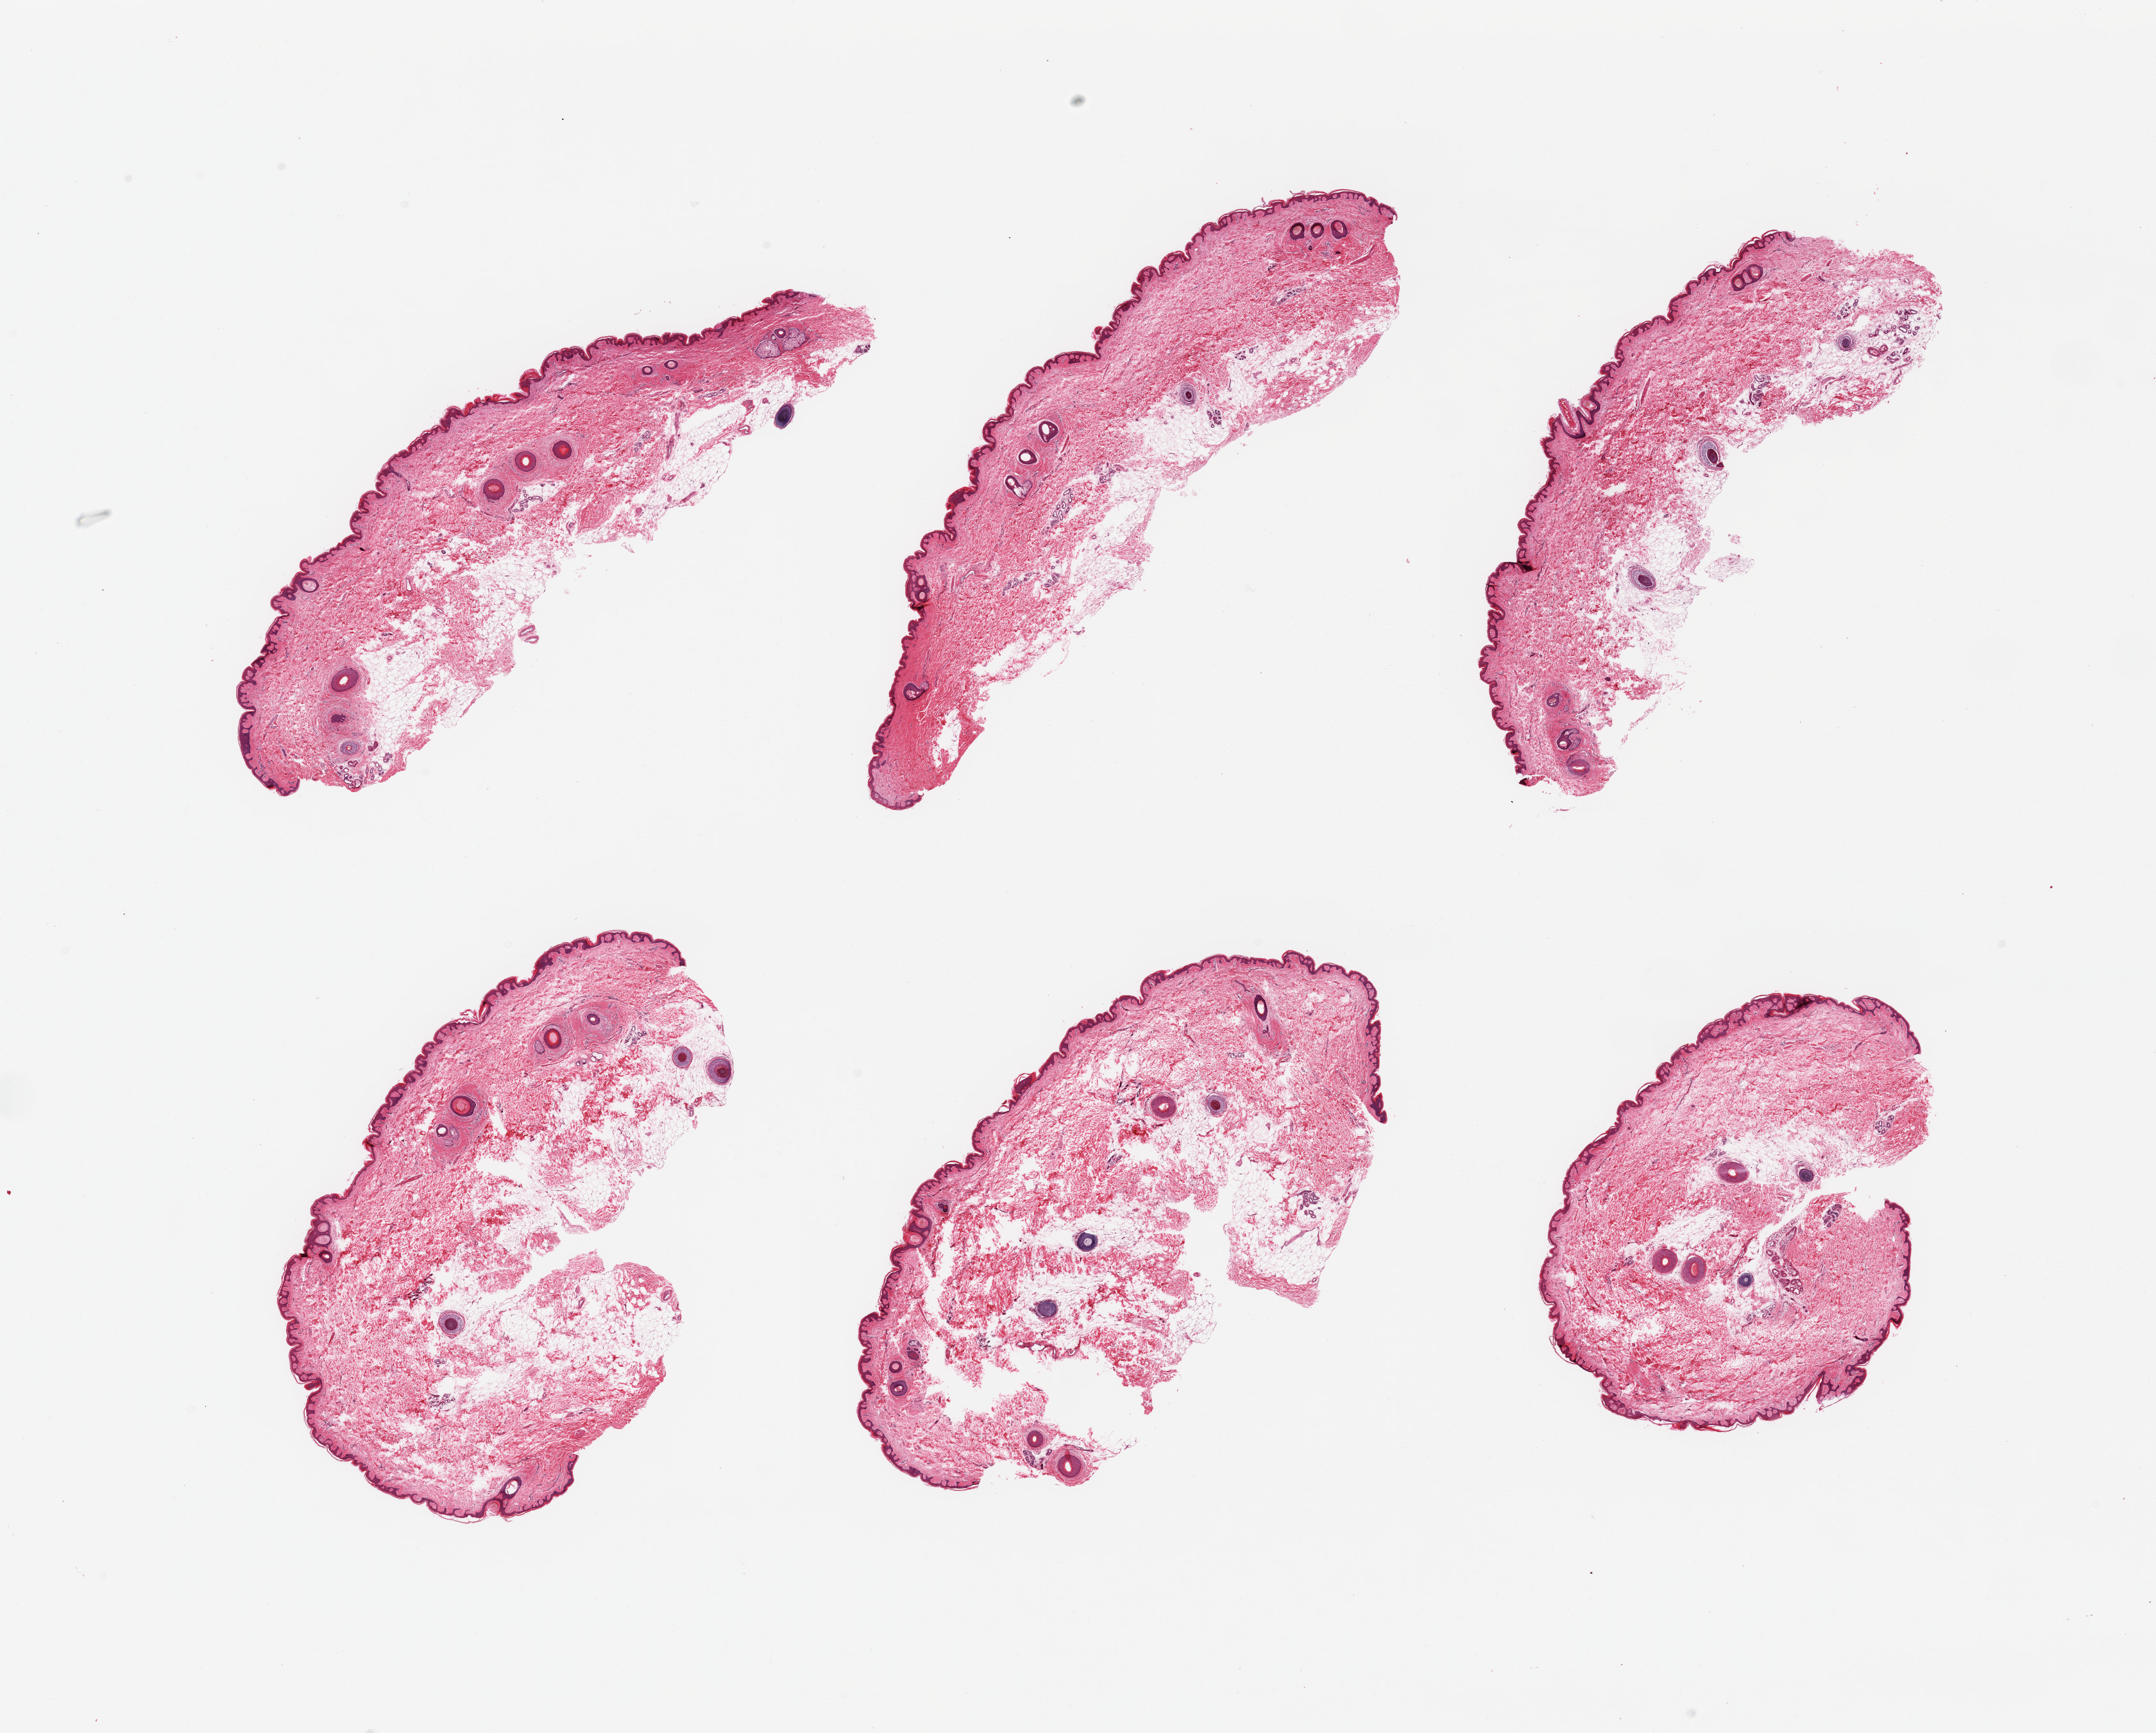
Digitized hematoxylin and eosin (H&E)-stained section, whole scanned area (about 26.6 x 21.4 mm) shown as a low-resolution overview, PAXgene-fixed paraffin-embedded (PFPE) section, section of skin of suprapubic region (target tissue), donor tissue sample.
Reviewer comment on this tissue sample: 6 pieces; hair bearing skin and internal/external fat up to 40%.